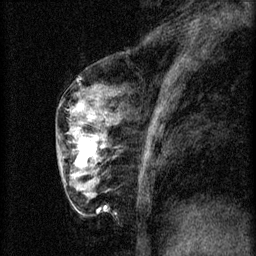
Breast MRI (dynamic contrast-enhanced), one sagittal slice. Position 24 of 60 along the scan axis. 3 images stored at this slice position (order not interpretable as contrast timing). 1.5 T. TE 4.2 ms, TR 8.2 ms. 2 mm slice thickness. 256 × 256 image matrix. Patient: female, 56 years.
Outlined on this slice (semi-automatically segmented with operator editing):
- analysis volume of interest (the breast-tissue region the enhancement analysis was run in; not a lesion): bounding box <60,124,114,179> (left, top, right, bottom; pixels)
- tumour enhancement mask (voxels above the 70 % enhancement threshold inside the analysis volume of interest): <76,138,105,167>